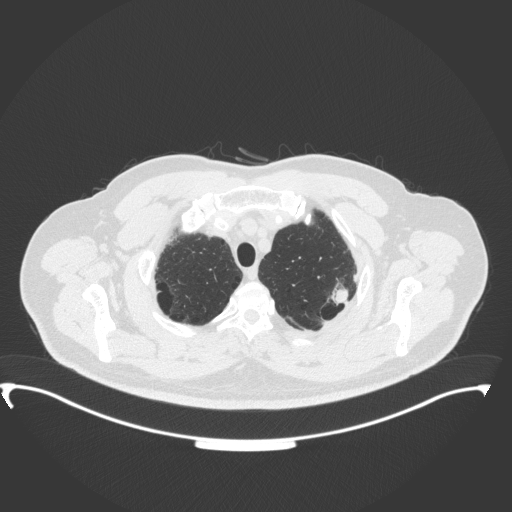
Chest CT, one axial slice. Slice 316 of 350 in the series (ordered by position). Reconstruction kernel B31f. Lung window (W 1500 / L -600 HU). 1 mm slice thickness. 512 × 512 image matrix, field of view 459 × 459 mm. Male patient, age 64 years. Case-level facts recorded for this patient, not image findings: clinical TNM (as recorded): T1c N1 M1.
Annotated regions visible in this slice (bounding box drawn by a radiologist):
- lung tumour (recorded histology: adenocarcinoma): bounding box <328,280,352,311> (left, top, right, bottom; pixels)